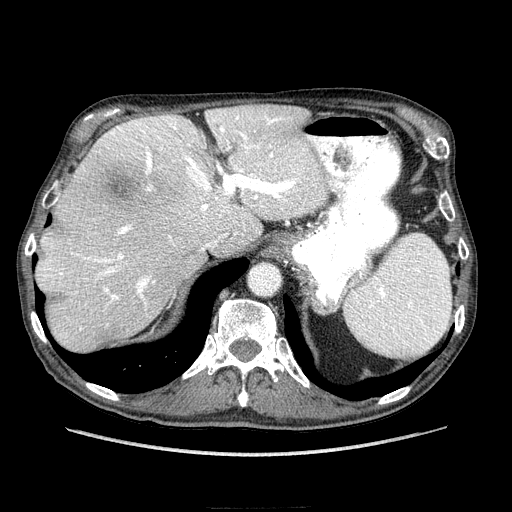
Contrast-enhanced abdominal CT (liver protocol), one axial slice. Position 169 of 218 along the scan axis. Soft-tissue window (W 400 / L 40 HU). 2.5 mm slice thickness. 512 × 512 image matrix. From the clinical record (not read from this slice): diagnosis: hepatocellular carcinoma (patient treated with transarterial chemoembolisation; whether this scan precedes or follows treatment is not stated here); TNM stage (as recorded): Stage-IIIA; Child-Pugh class: A.
Outlined on this slice (semi-automatically segmented with operator editing):
- abdominal aorta: box from (x=251, y=264) to (x=280, y=295) px
- liver parenchyma outside the tumour (the mass and vessels are separate outlines, so this box may not span the whole liver): (x=38, y=106)–(x=326, y=352)
- mass: (x=92, y=162)–(x=144, y=212)
- liver vessels: (x=39, y=111)–(x=324, y=331)